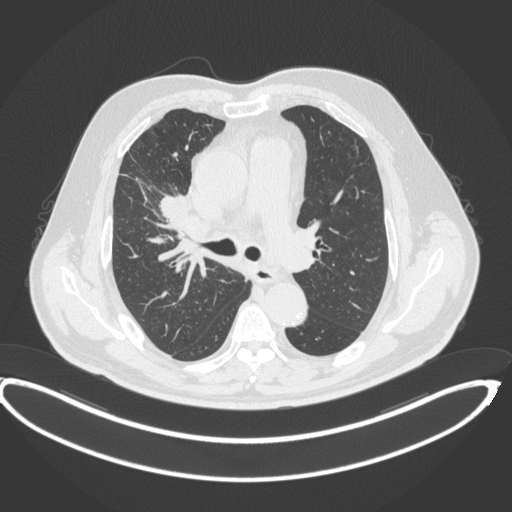
Chest CT, one axial slice. Reconstruction kernel B31f. Lung window (W 1500 / L -600 HU). 512 × 512 image matrix. Male patient, age 62 years. From the clinical record (not read from this slice): clinical TNM (as recorded): T1c N3 M1c.
Outlined on this slice (rectangle marked by the reading radiologist):
- lung tumour (recorded histology: adenocarcinoma): bounding box (x1, y1, x2, y2) in pixels: (155, 190, 192, 219)